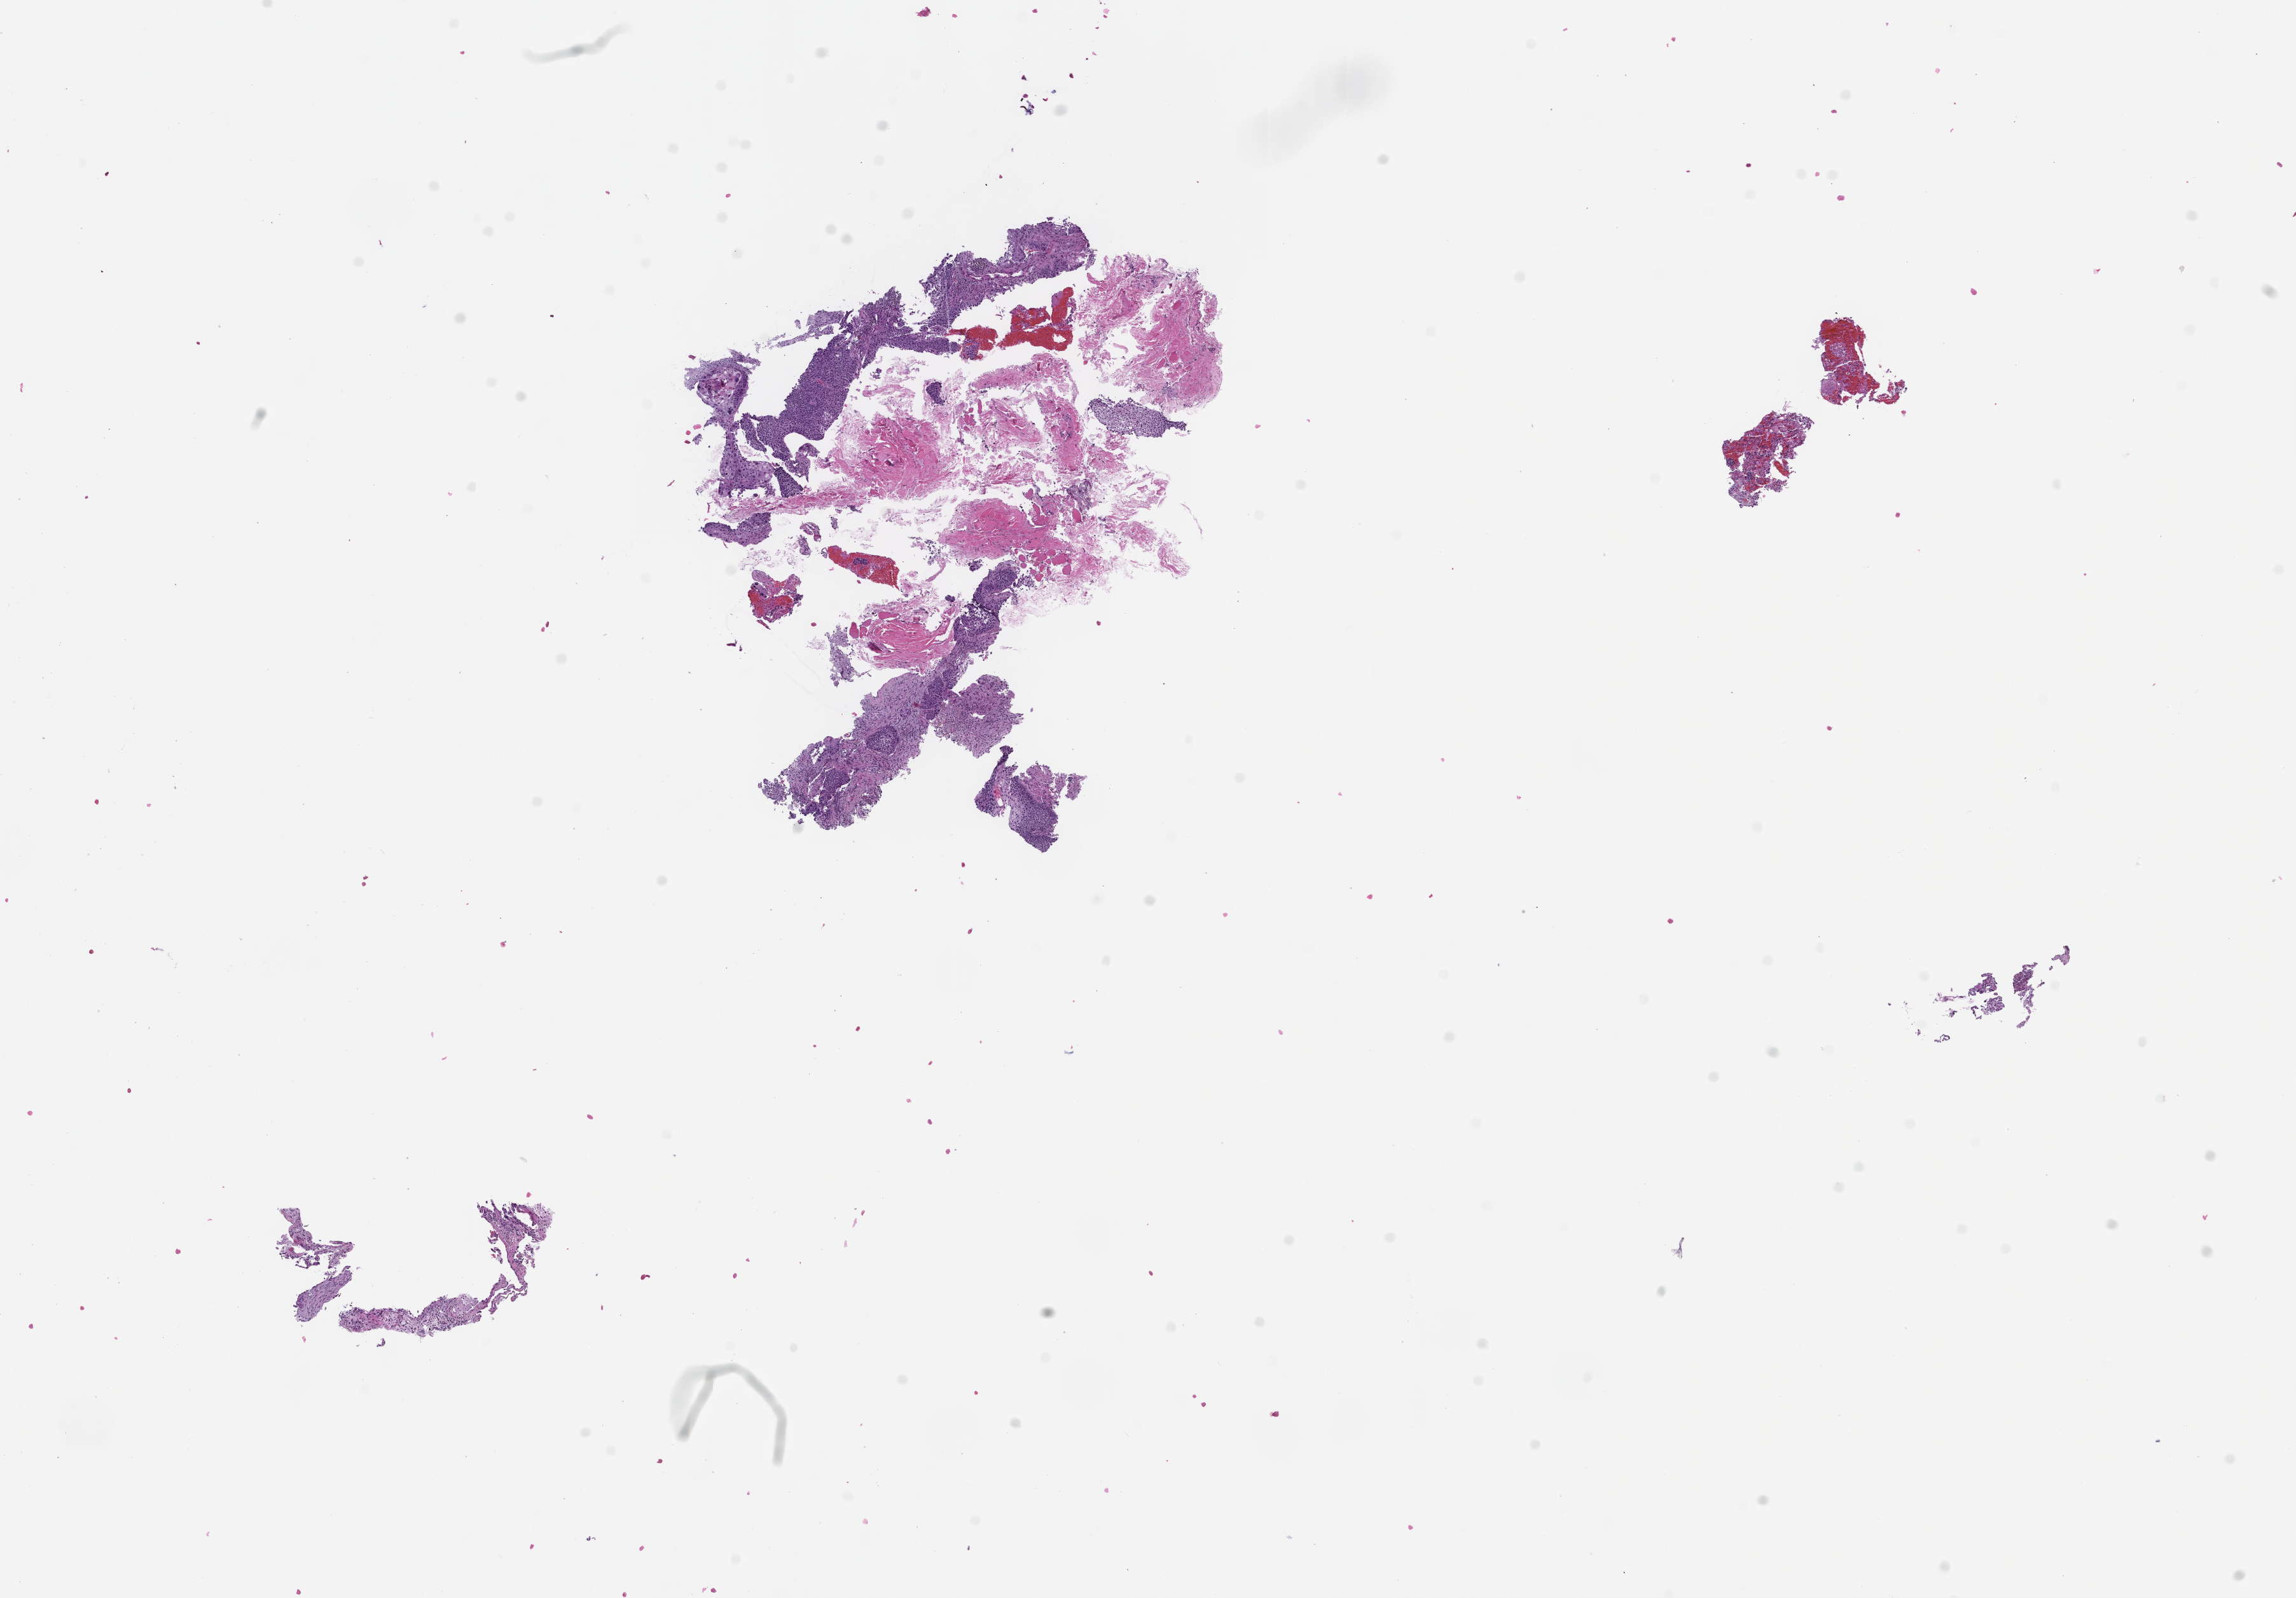
Digitized hematoxylin and eosin (H&E)-stained section — a low-resolution overview of the entire scanned area, about 14.6 x 10.1 mm. Paraffin-embedded section. Tissue site: lung. Patient sex: female.
This section: primary tumour tissue. Diagnosis: Non-Small Cell Lung Carcinoma.